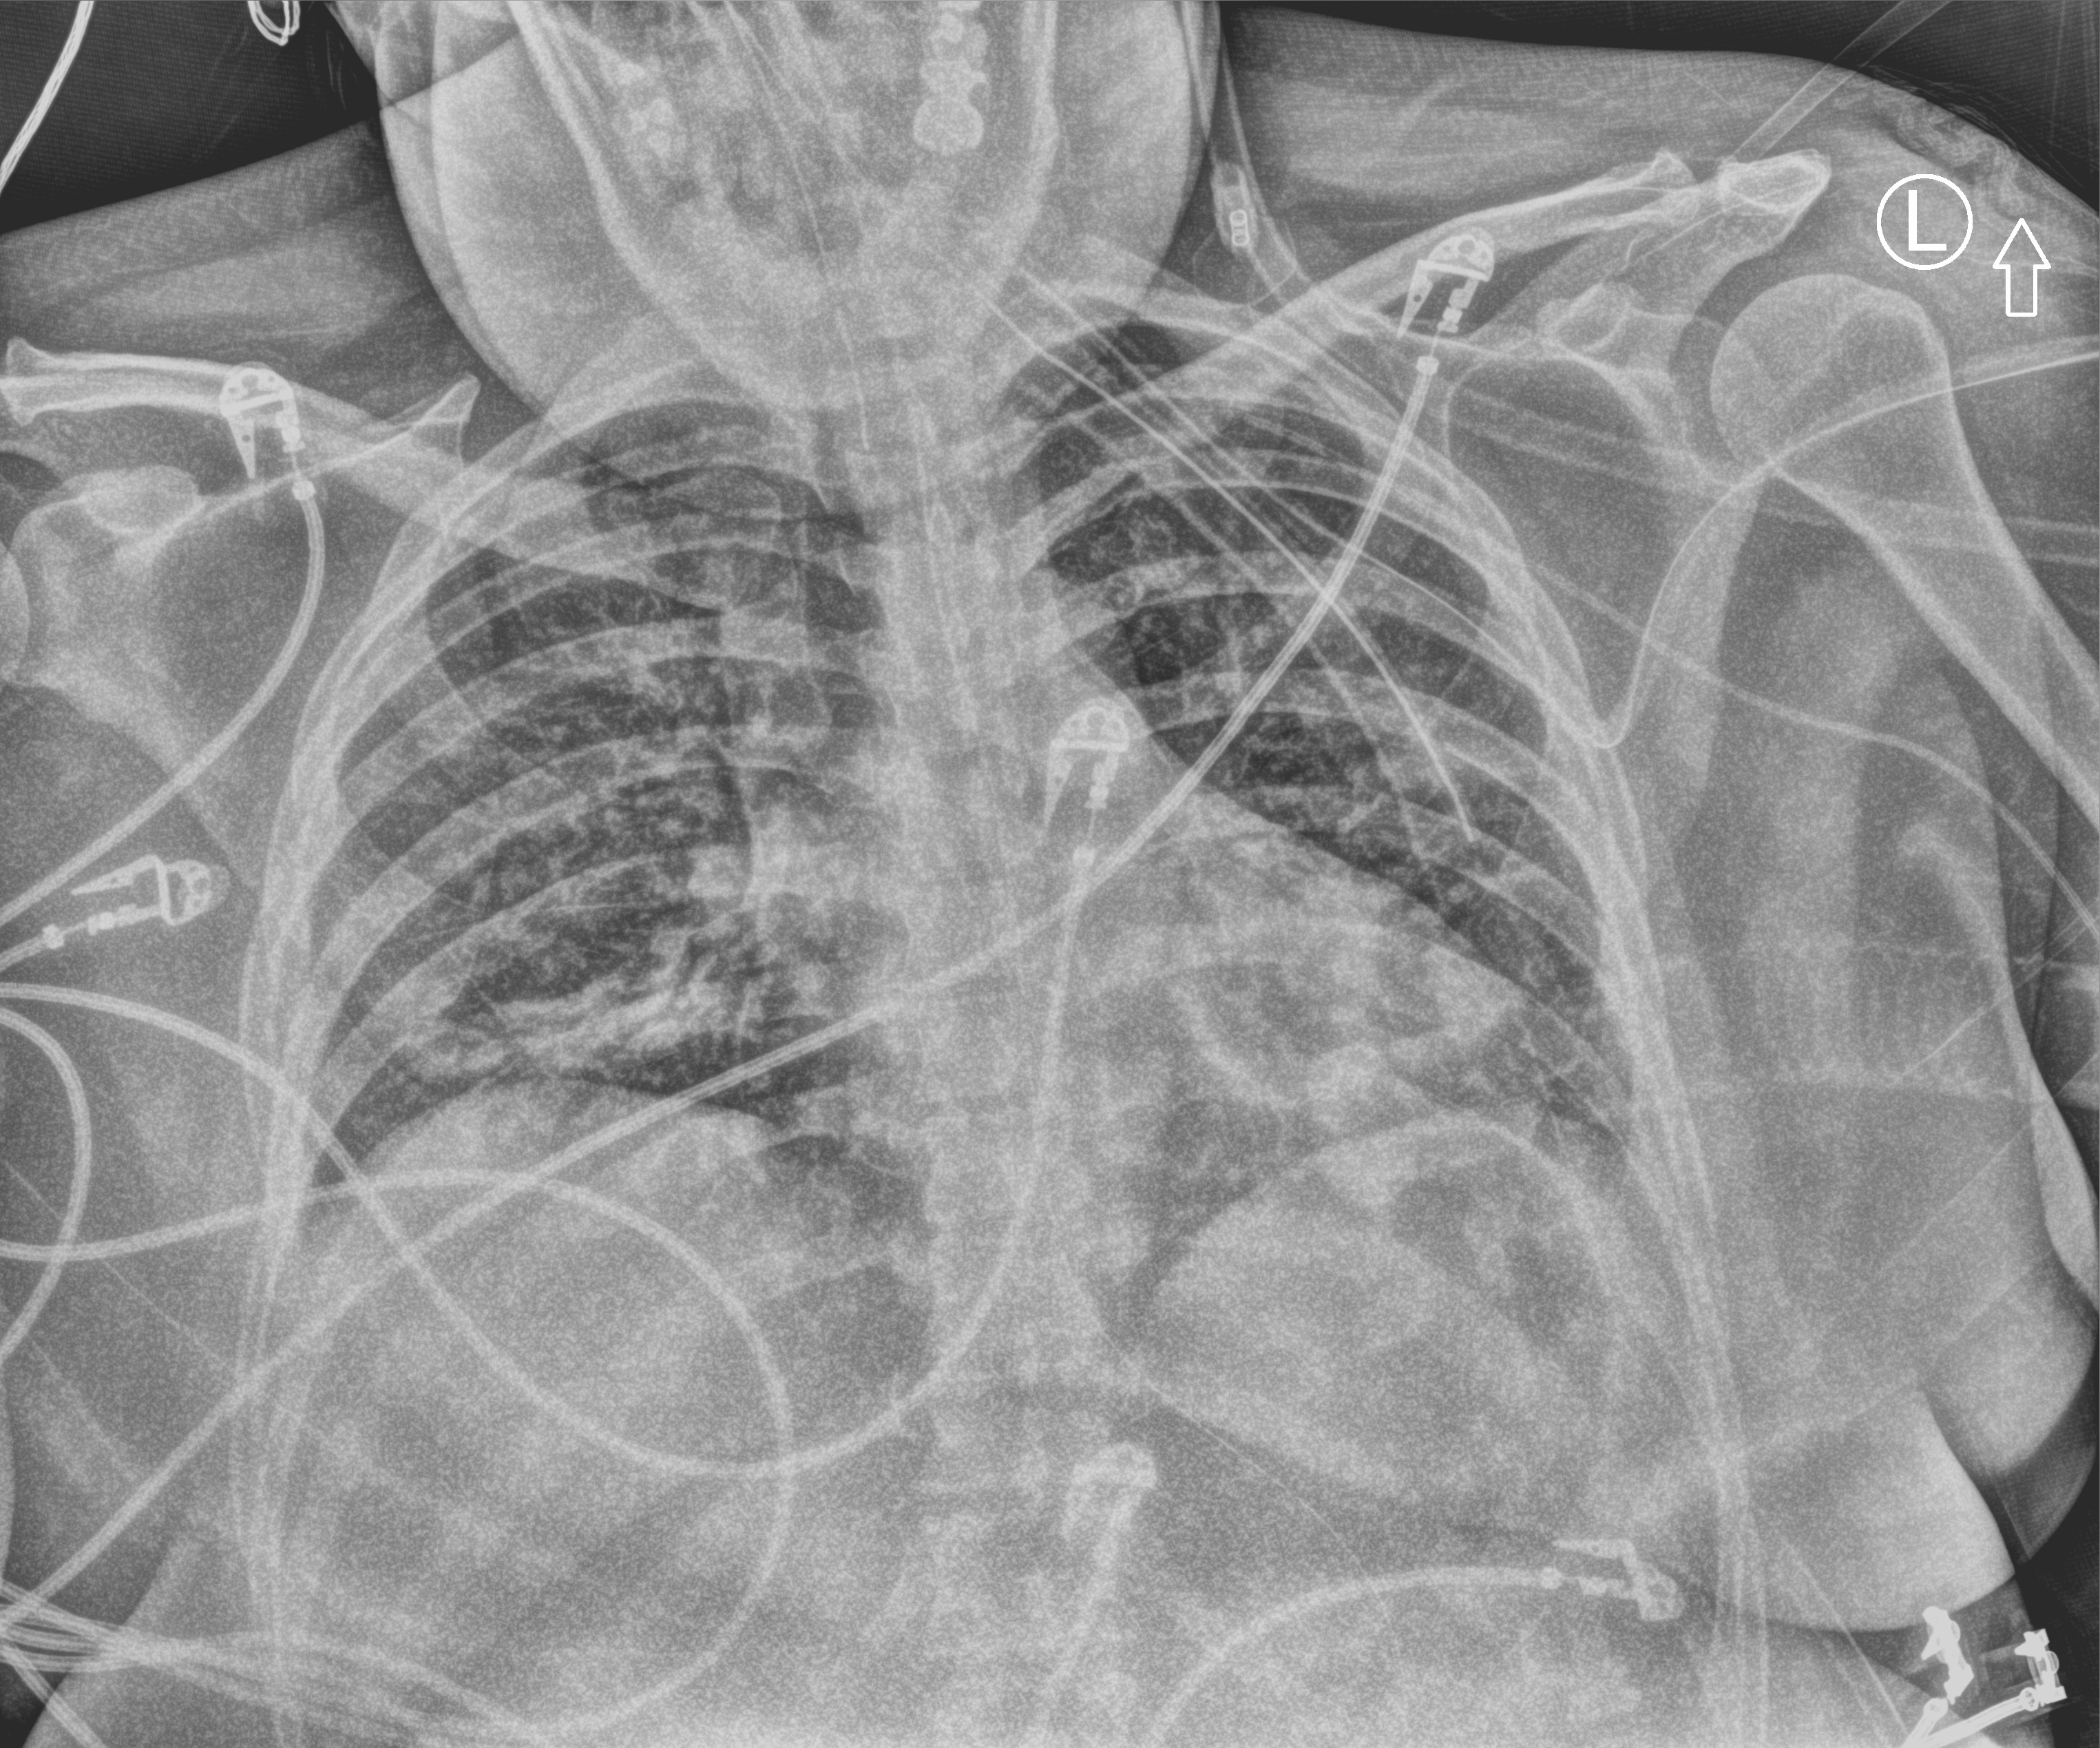
Bedside chest radiograph (computed radiography); anteroposterior (AP) projection. Patient hospitalised with COVID-19; female, aged 18–59 years.
From the hospital-stay record, not from the radiograph (when in the stay this image was taken is not recorded): smoking status (admission record): never; mechanically ventilated during this hospital stay: yes; admitted to intensive care during this hospital stay: no.